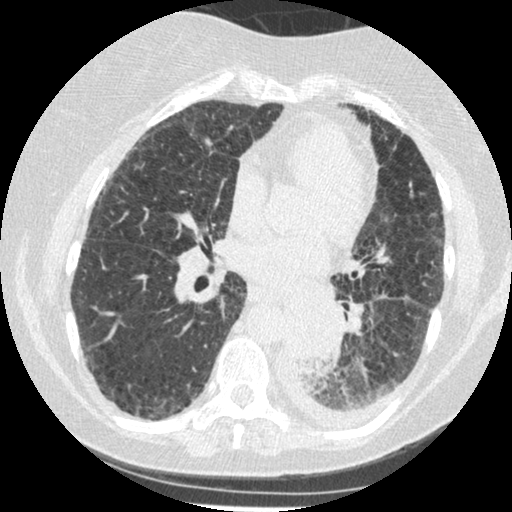
Axial slice from a low-dose chest CT screening exam; third annual screen; lung window (W 1500 / L -600 HU); slice 232 of 341 in the series. Female participant, aged 60 years at enrolment. Former smoker at enrolment.
• Expert reader's lesion annotation, bounding box <275,304,343,375> (left, top, right, bottom; pixels).
• Screening reader's record for this exam (one nodule recorded; not confirmed to be the boxed lesion): non-calcified nodule or mass ≥4 mm, left lower lobe, 54 × 38 mm, smooth margins, soft tissue attenuation, pre-existing on the prior screen: yes; interval growth: yes.
• Official screen result: positive, other.
• Lung cancer was diagnosed 15 days after this screen: small cell carcinoma, NOS, left lower lobe, undifferentiated (G4), stage IV (AJCC 6th edition), 69 mm at pathology.